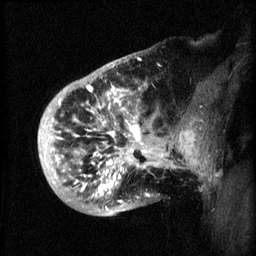
Breast MRI (dynamic contrast-enhanced), one sagittal slice; slice 13 of 60 in the series (ordered by position); 3 images stored at this slice position (order not interpretable as contrast timing); 1.5 T; TE 4.2 ms, TR 8.2 ms; 256 × 256 image matrix, field of view 200 × 200 mm. Female patient, age 50 years.
Outlined on this slice (semi-automatically segmented with operator editing):
- analysis volume of interest (the breast-tissue region the enhancement analysis was run in; not a lesion): bounding box (x1, y1, x2, y2) in pixels: (44, 72, 173, 217)
- tumour enhancement mask (voxels above the 70 % enhancement threshold inside the analysis volume of interest): (45, 86, 172, 211)